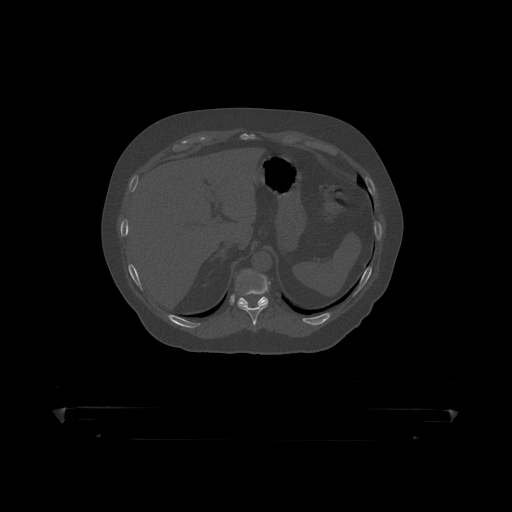
CT including the spine, one axial slice; position 208 of 390 along the scan axis; reconstruction kernel STANDARD; bone window (W 1800 / L 400 HU); 1.25 mm slice thickness; 512 × 512 image matrix. Male patient, age 60 years. From the clinical record (not read from this slice): primary cancer: prostate.
Structures marked on this image (semi-automatically segmented with operator editing):
- T10 vertebra: bounding box <238,275,271,319> (left, top, right, bottom; pixels)
- T11 vertebra: <238,274,268,306>